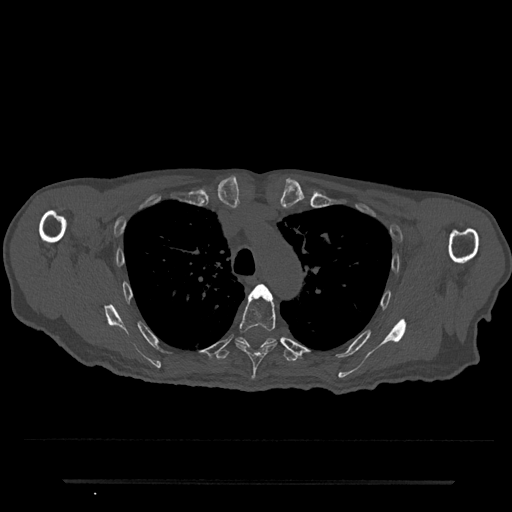
CT including the spine, one axial slice; slice 568 of 797 in the series (ordered by position); reconstruction kernel Br40s/3; 120 kVp; bone window (W 1800 / L 400 HU); 512 × 512 image matrix. Patient: male, 74 years. From the clinical record (not read from this slice): primary cancer: prostate.
Structures marked on this image (semi-automatic segmentation, software-assisted and operator-edited):
- T4 vertebra: bounding box (x1, y1, x2, y2) in pixels: (257, 284, 264, 289)
- T5 vertebra: (236, 285, 277, 380)
- T6 vertebra: (215, 337, 299, 362)